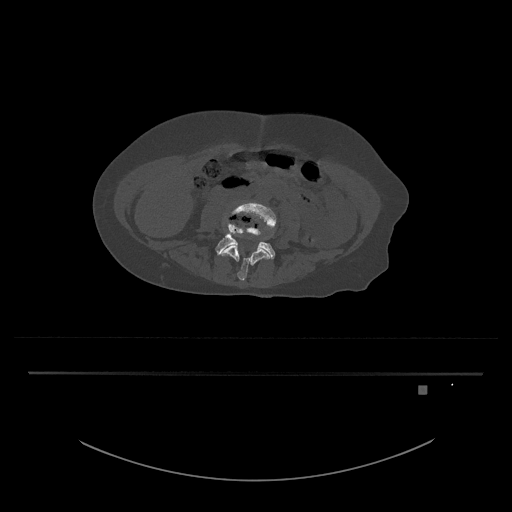
CT including the spine, one axial slice; position 336 of 797 along the scan axis; reconstruction kernel Br40s/3; 120 kVp; bone window (W 1800 / L 400 HU); 0.5 mm slice thickness; 512 × 512 image matrix, field of view 500 × 500 mm. Patient: female, 57 years. Case-level facts recorded for this patient, not image findings: primary cancer: cervical.
Annotated regions visible in this slice (semi-automatic segmentation, software-assisted and operator-edited):
- L4 vertebra: bounding box <220,201,277,281> (left, top, right, bottom; pixels)